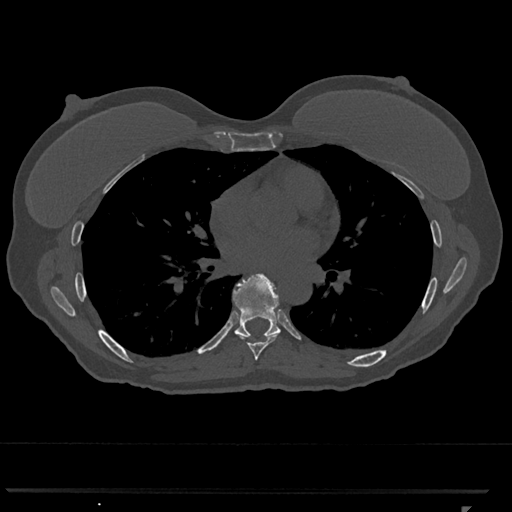
CT including the spine, one axial slice; position 690 of 793 along the scan axis; 120 kVp; bone window (W 1800 / L 400 HU); 512 × 512 image matrix. Patient: female, 62 years. Case-level facts recorded for this patient, not image findings: primary cancer: renal.
Annotated regions visible in this slice (semi-automatic segmentation, software-assisted and operator-edited):
- T7 vertebra: bounding box (x1, y1, x2, y2) in pixels: (238, 333, 279, 361)
- T8 vertebra: (233, 274, 281, 338)